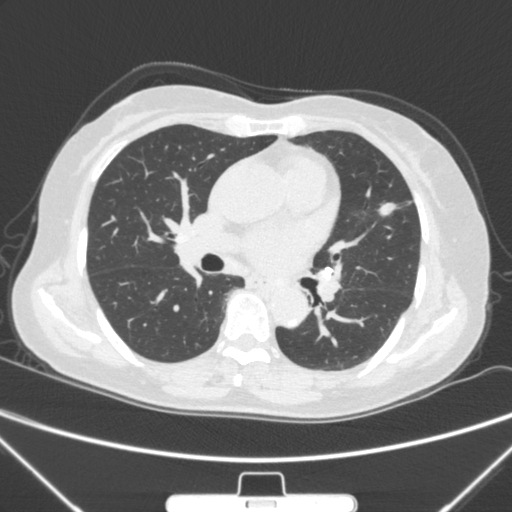
Chest CT, one axial slice; position 150 of 300 along the scan axis; lung window (W 1500 / L -600 HU); 512 × 512 image matrix, field of view 350 × 350 mm. Patient: female, 70 years. From the clinical record (not read from this slice): clinical TNM (as recorded): T1b N0 M0; histopathological grade: G2.
Annotated regions visible in this slice (rectangle marked by the reading radiologist):
- lung tumour (recorded histology: adenocarcinoma): bounding box (x1, y1, x2, y2) in pixels: (377, 193, 404, 230)